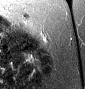
MRI of an extremity soft-tissue mass, one axial slice; T2-weighted fat-saturated; MR volume resampled by the dataset authors to the PET/CT grid (not the native acquisition matrix); 3.27 mm slice thickness; 85 × 89 image matrix, field of view 83 × 87 mm. Female patient. From the clinical record (not read from this slice): histological type: leiomyosarcoma; grade: intermediate; site of the primary tumour: parascapusular.
Structures marked on this image (expert contour drawn on MRI and transferred to this co-registered scan by the dataset authors):
- gross tumour volume including surrounding oedema: bounding box (x1, y1, x2, y2) in pixels: (27, 26, 37, 35)
- gross tumour volume (mass): (29, 28, 35, 31)